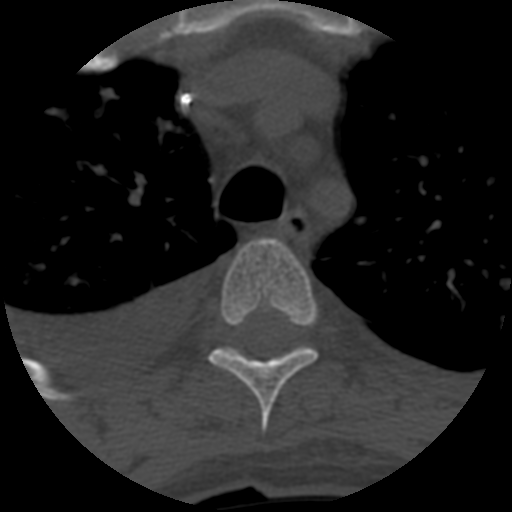
CT including the spine, one axial slice; position 469 of 708 along the scan axis; reconstruction kernel STANDARD; one of 3 acquisitions stored at this slice position; bone window (W 1800 / L 400 HU); 1.25 mm slice thickness; 512 × 512 image matrix. Patient age 55 years. From the clinical record (not read from this slice): primary cancer: colon; vertebrae with lytic lesions (as recorded): T12, L1, L5.
Outlined on this slice (semi-automatically segmented with operator editing):
- T4 vertebra: bounding box <208,238,319,433> (left, top, right, bottom; pixels)
- T5 vertebra: <219,347,311,355>